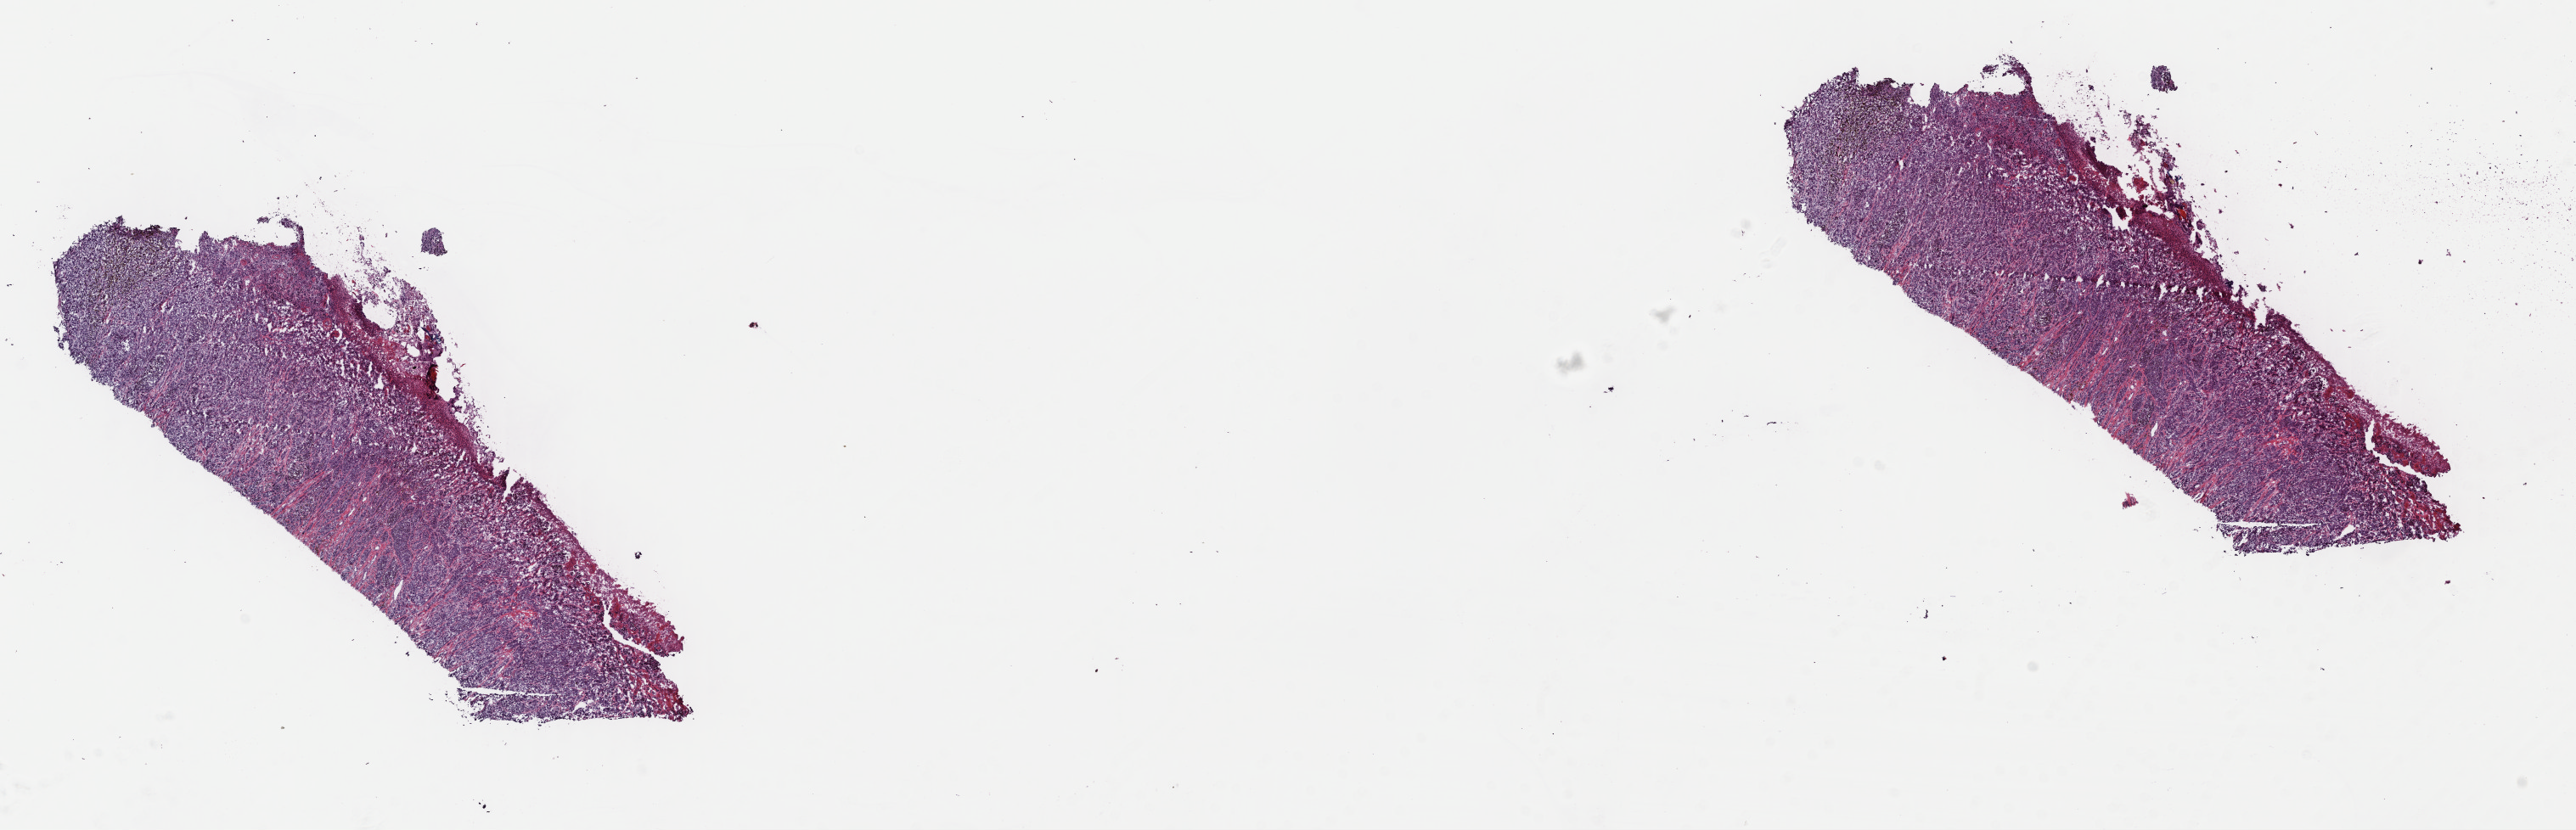
Digitized H&E tissue section (whole slide), shown as a low-resolution overview of the whole scanned area (about 23.8 x 7.7 mm, slide scanned at 40x), frozen section from the top of the tissue portion, sample: primary tumour, skin. Male patient; age at initial diagnosis 56 years. Composition of this section per pathologist review: tumour cells 80%, tumour nuclei 90%, normal cells 0%, stromal cells 10%, necrosis 10%. Infiltration values recorded for this section: lymphocyte infiltration 5%, monocyte infiltration 0%, neutrophil infiltration 0%.
TNM: T4b N1 M0. AJCC pathologic stage: IIIB (7th edition). Pathologic diagnosis: Malignant melanoma, NOS.